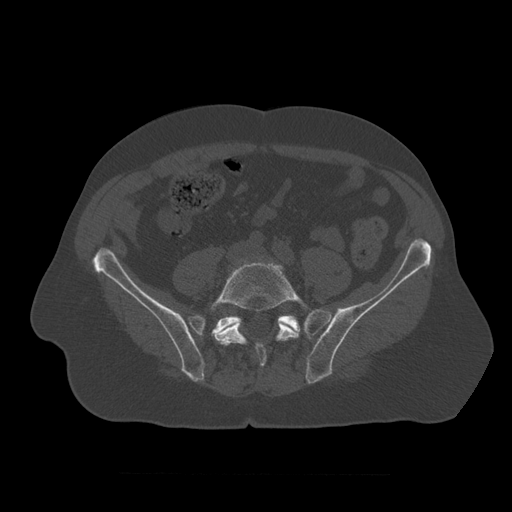
CT including the spine, one axial slice; slice 251 of 450 in the series (ordered by position); 120 kVp; bone window (W 1800 / L 400 HU); 1.25 mm slice thickness; 512 × 512 image matrix. Patient age 75 years. Case-level facts recorded for this patient, not image findings: primary cancer: prostate.
Annotated regions visible in this slice (semi-automatic segmentation, software-assisted and operator-edited):
- L5 vertebra: bounding box (x1, y1, x2, y2) in pixels: (211, 261, 309, 367)